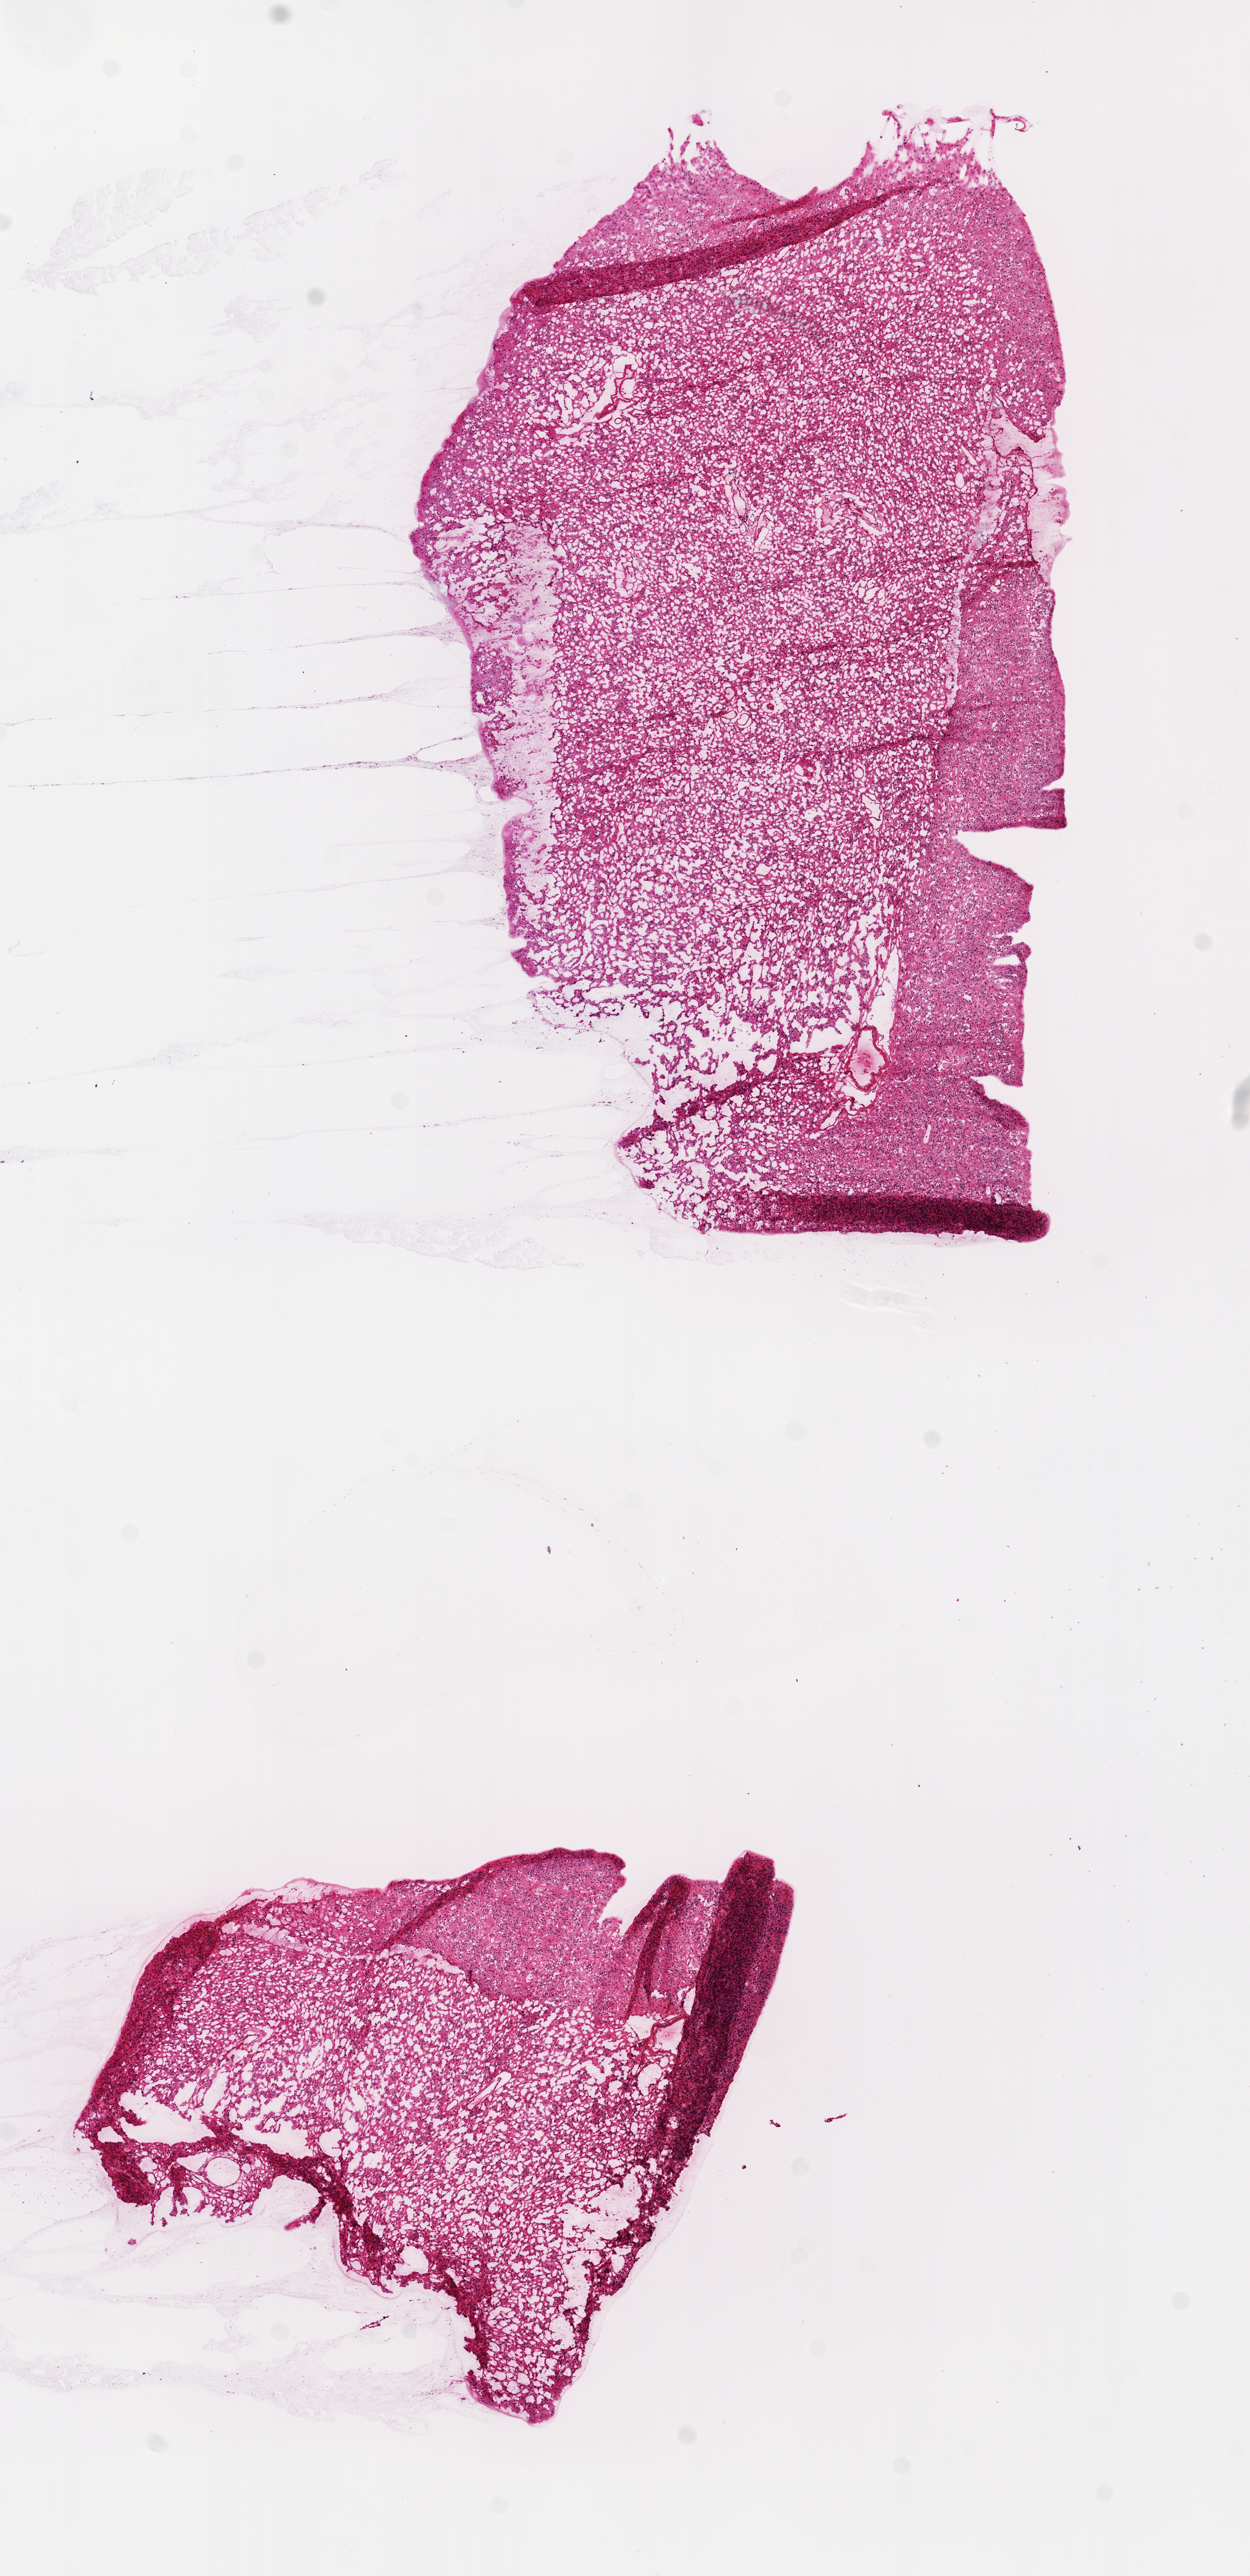
Digitized H&E-stained tissue section (whole slide), shown as a low-resolution overview of the whole scanned area (about 6.0 x 12.4 mm, acquisition: 20x scan). Frozen section. Brain, primary tumour sample. Male, age 32 years at initial diagnosis. Composition of this section per pathologist review: tumour cells 100%, tumour nuclei 75%.
Histologic diagnosis: Oligodendroglioma, anaplastic (cerebrum).